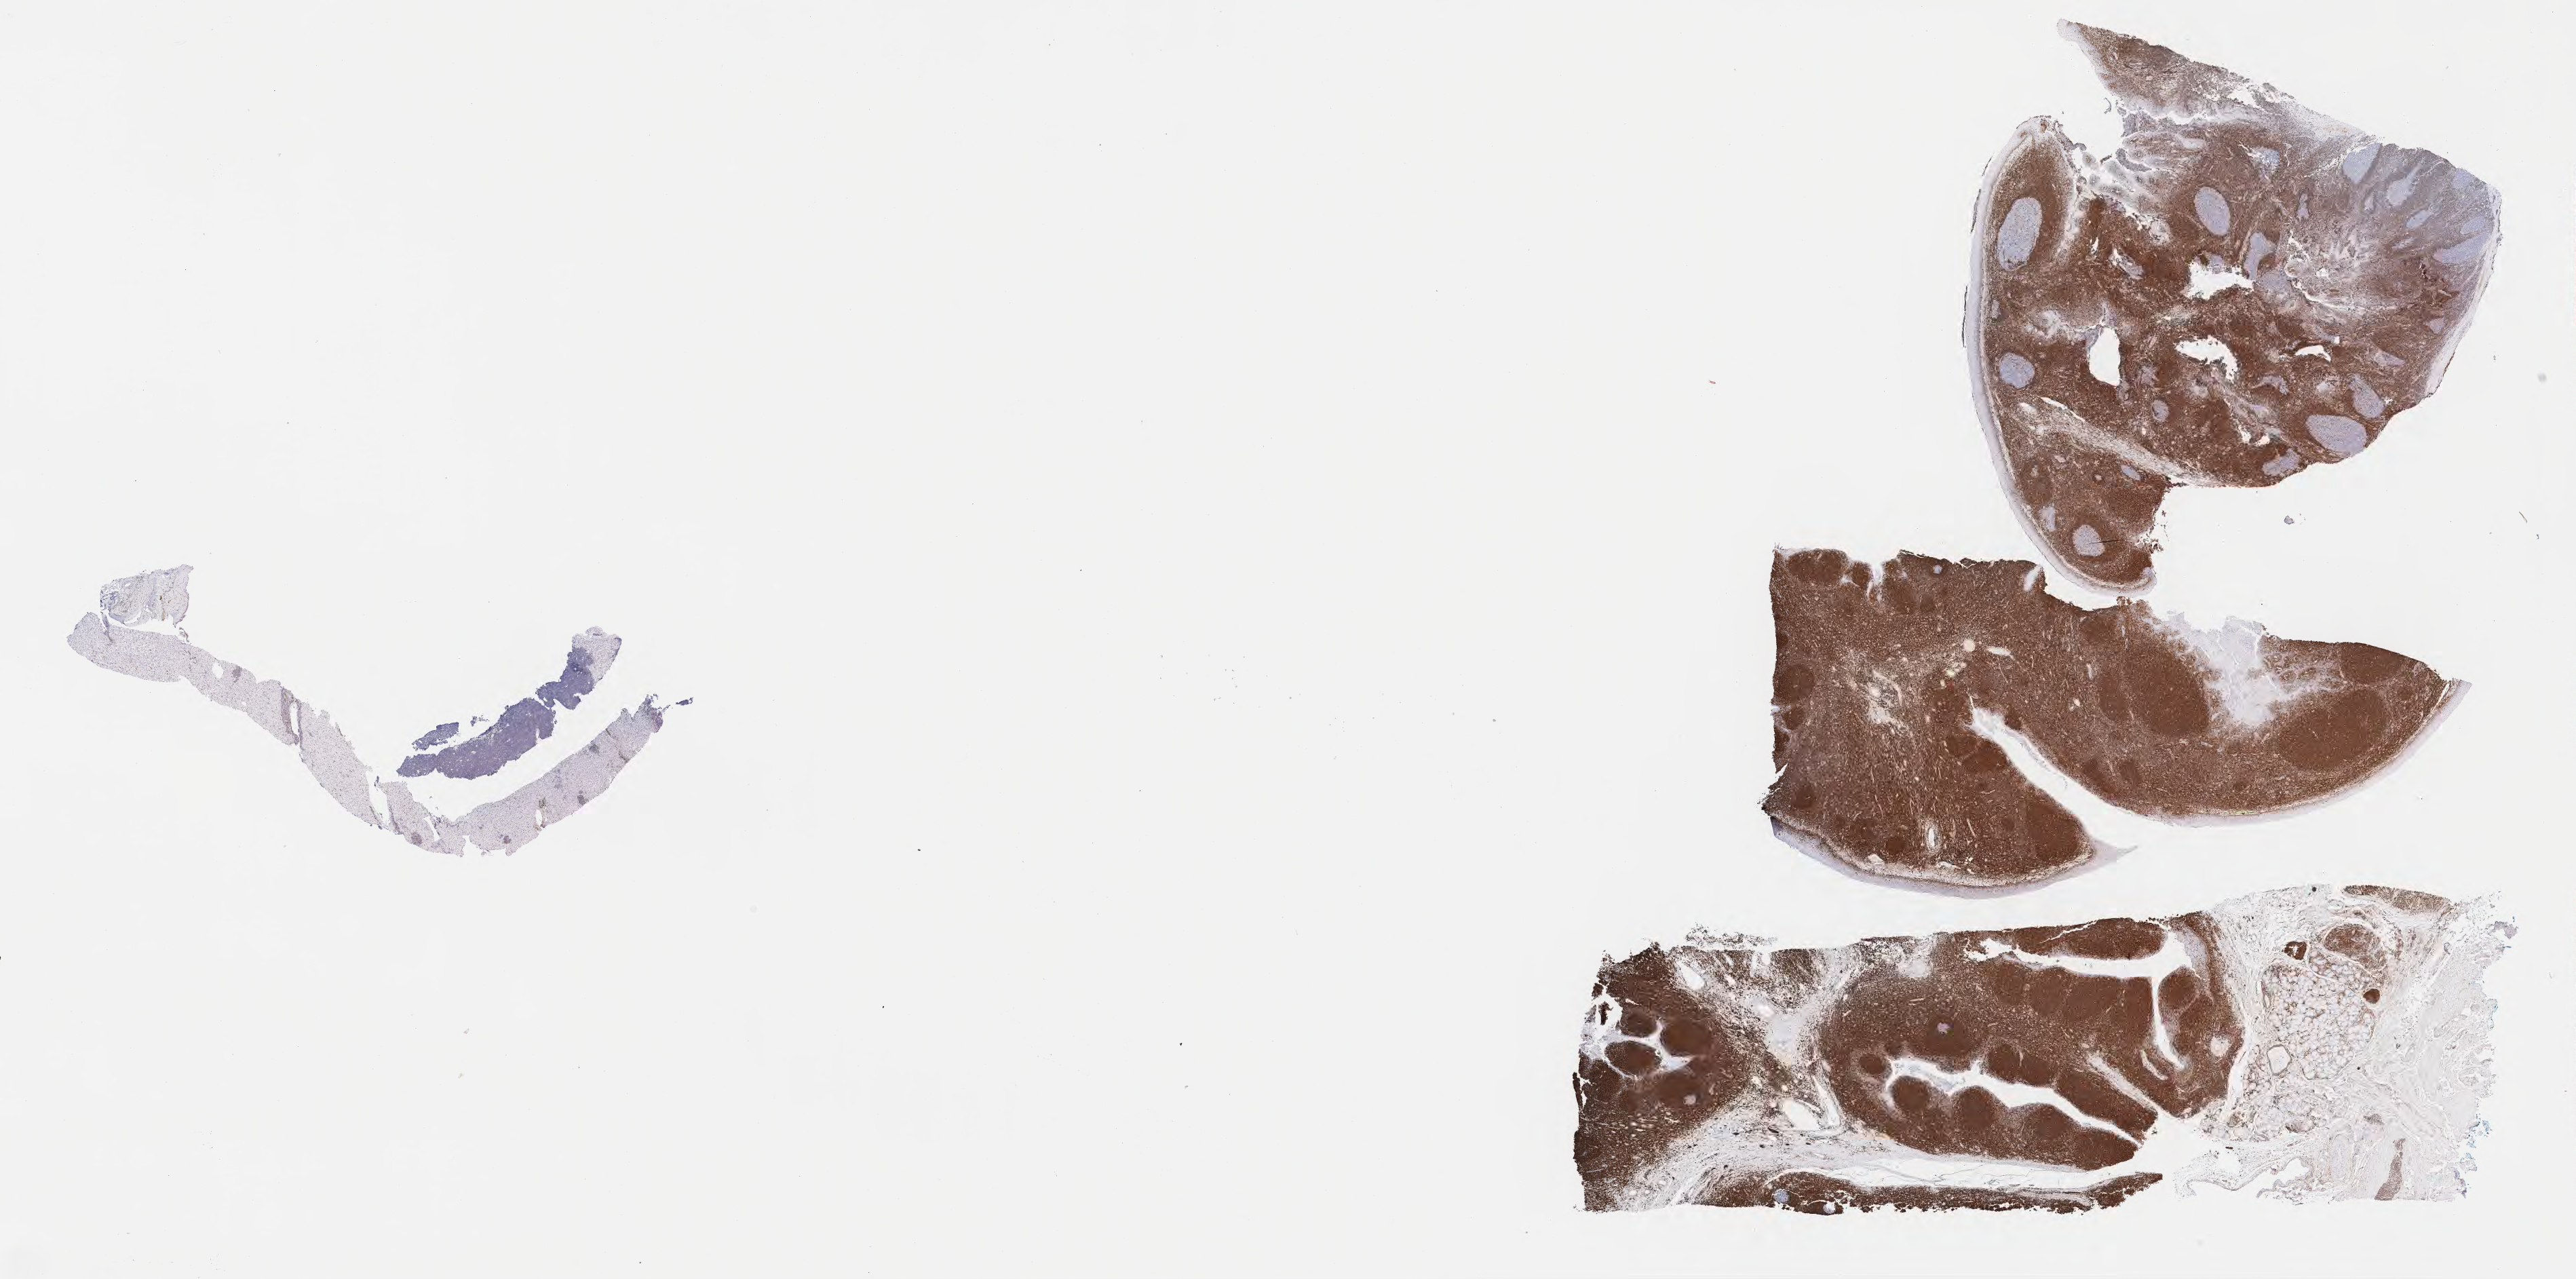
IHC for BCL2, whole-slide image, shown as a low-resolution overview of the whole scanned area (about 30.7 x 15.2 mm). Tumor tissue. Anatomic site: liver. Male, age 7 years at initial diagnosis.
Histologic diagnosis: Burkitt lymphoma, NOS.